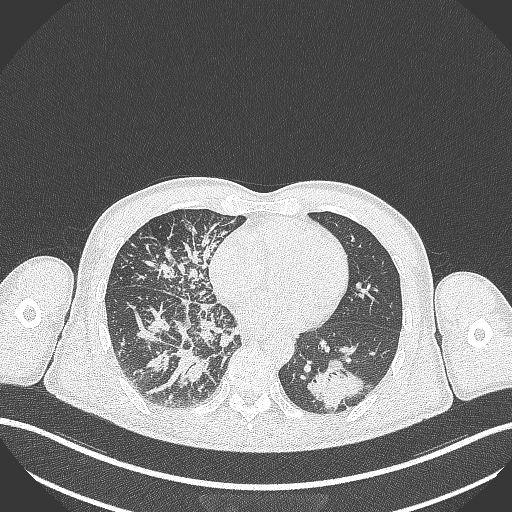
Chest CT, one axial slice; slice 120 of 348 in the series (ordered by position); reconstruction kernel B70f; lung window (W 1500 / L -600 HU); 512 × 512 image matrix. Male patient, age 49 years. Case-level facts recorded for this patient, not image findings: clinical TNM (as recorded): T2b N1 M0.
Structures marked on this image (bounding box drawn by a radiologist):
- lung tumour (recorded histology: adenocarcinoma): bounding box [x1, y1, x2, y2] px = [303, 357, 367, 410]